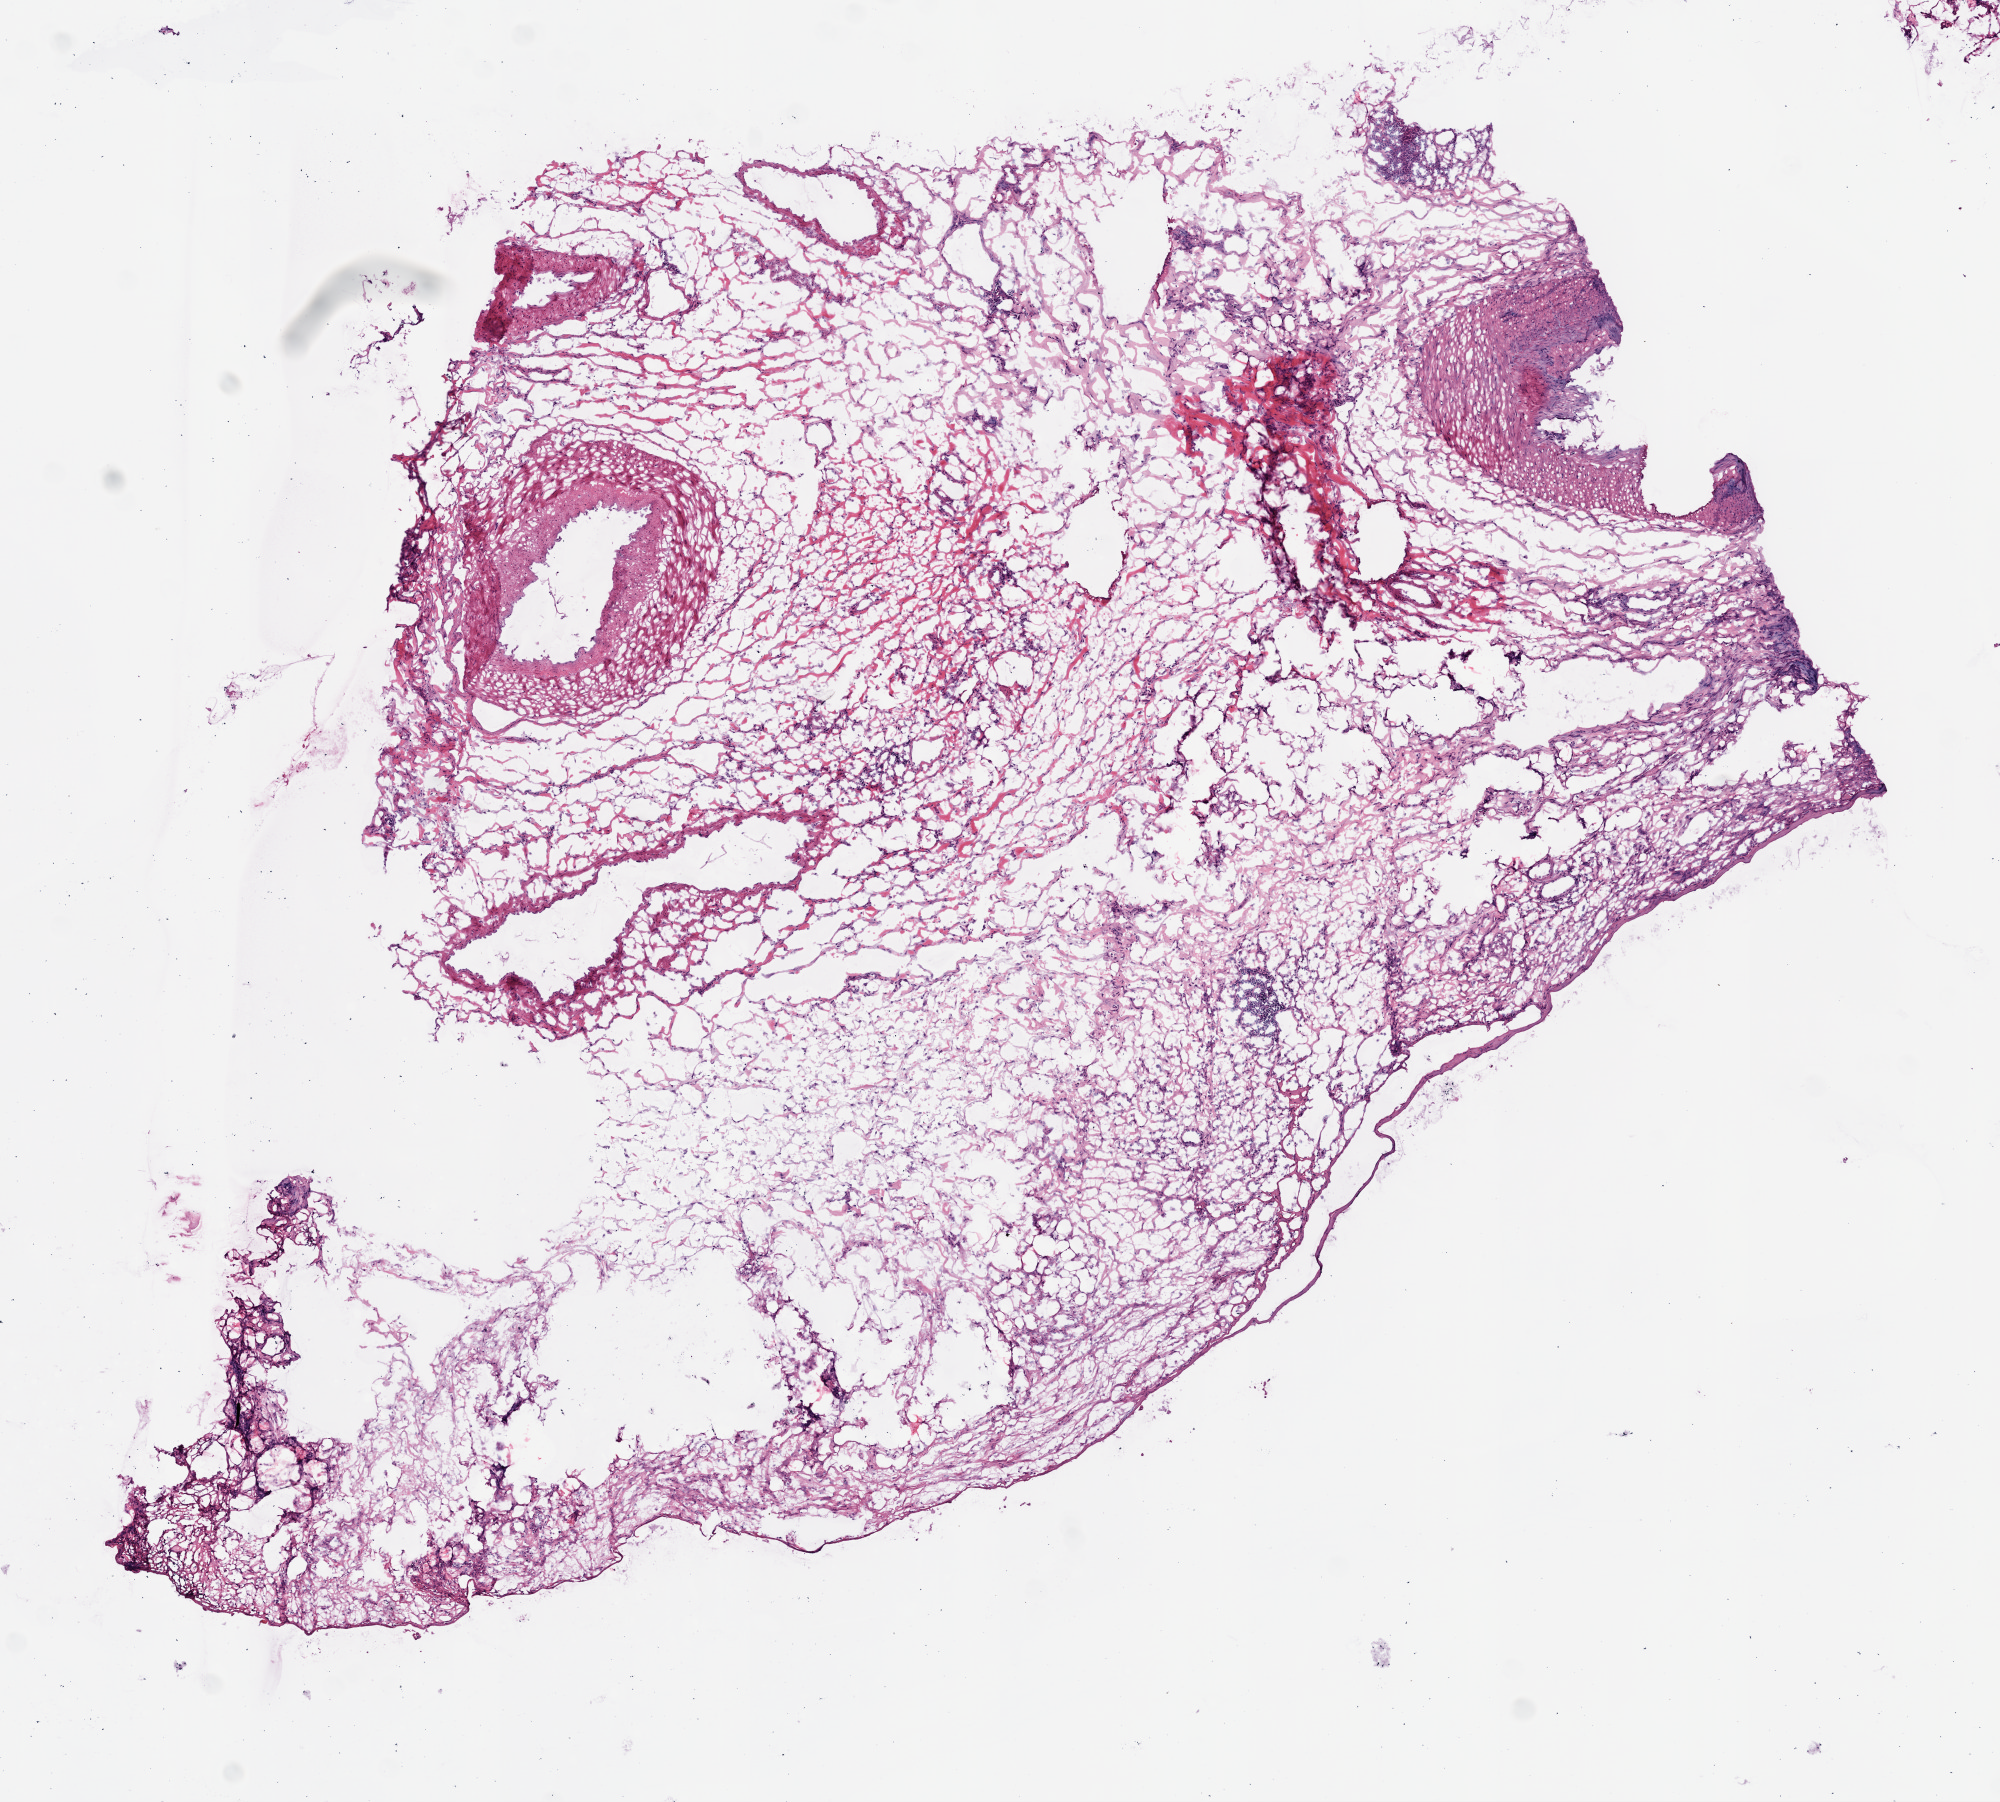
Whole-slide histology image, H&E, low-resolution overview of the scanned area, about 8.0 x 7.2 mm (acquisition: 20x scan), frozen section from the top of the tissue portion, stomach, primary tumour sample. Female patient; age at initial diagnosis 64 years. Histologic grade: G3 (poorly differentiated). Pathologist review of this section (percent, as recorded): tumour cells 99%, tumour nuclei 90%, normal cells 0%, stromal cells 0%, necrosis 1%. Infiltration values recorded for this section: lymphocyte infiltration 2%, monocyte infiltration 2%, neutrophil infiltration 0%.
* pathologic diagnosis: Adenocarcinoma, NOS (gastric antrum)
* AJCC pathologic stage: IIA (7th edition)
* lymph nodes positive (case pathology): 0 of 15 examined